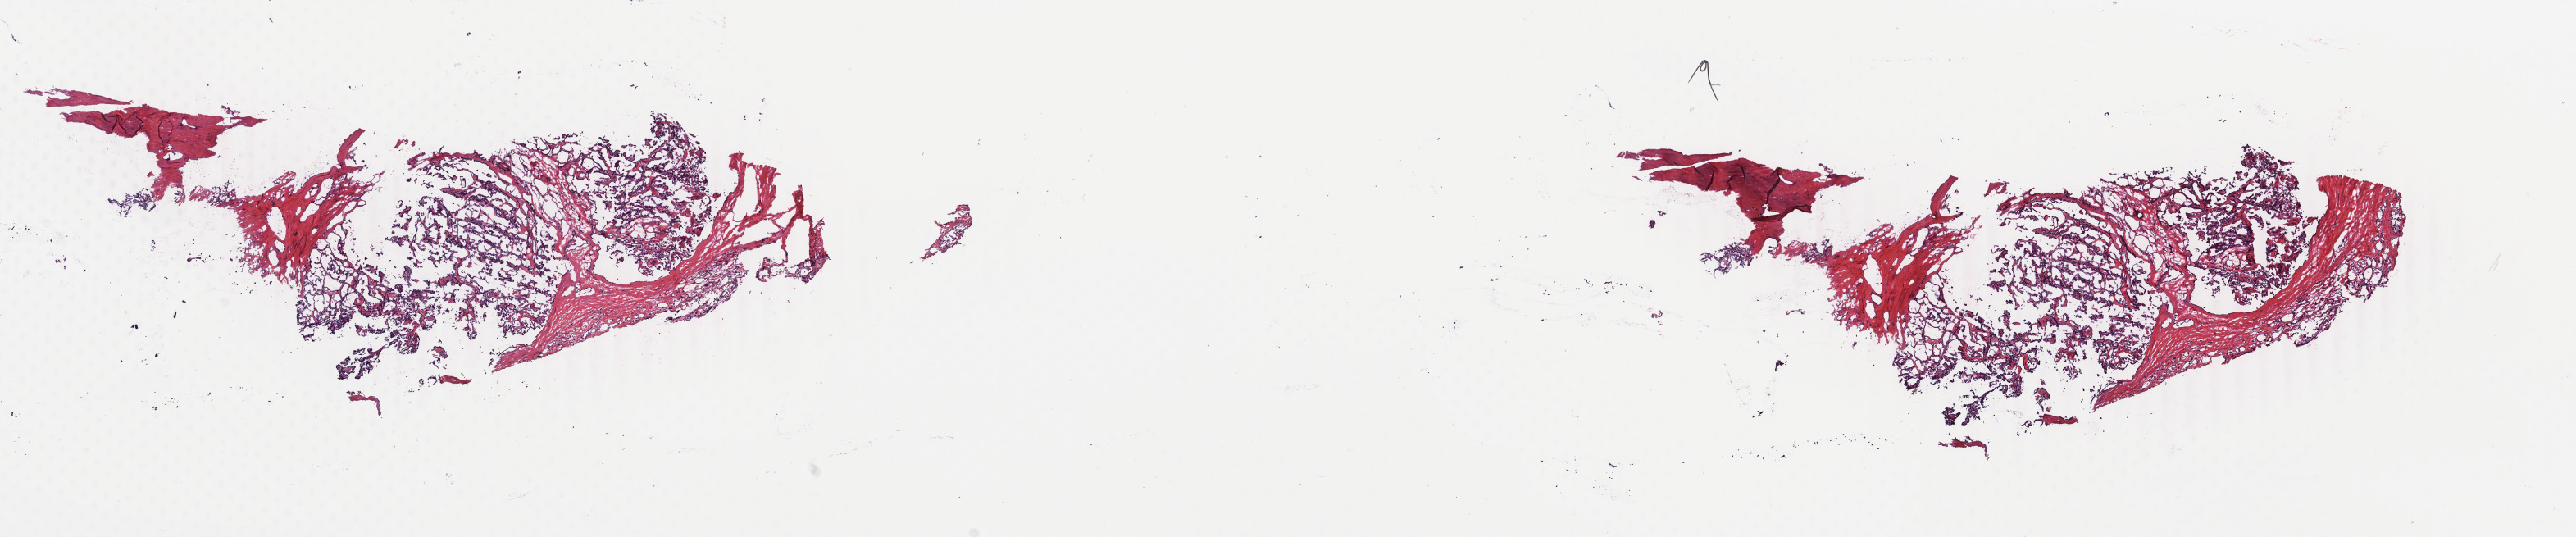
Digitized H&E-stained tissue section (whole slide) — whole scanned area (about 25.0 x 5.2 mm) shown as a low-resolution overview, frozen section from the top of the tissue portion, thyroid, primary tumour sample. Patient: male, age at initial diagnosis 41 years. Slide review estimates, as recorded: tumour cells 85%, tumour nuclei 85%.
Histologic diagnosis: Papillary adenocarcinoma, NOS (thyroid gland).